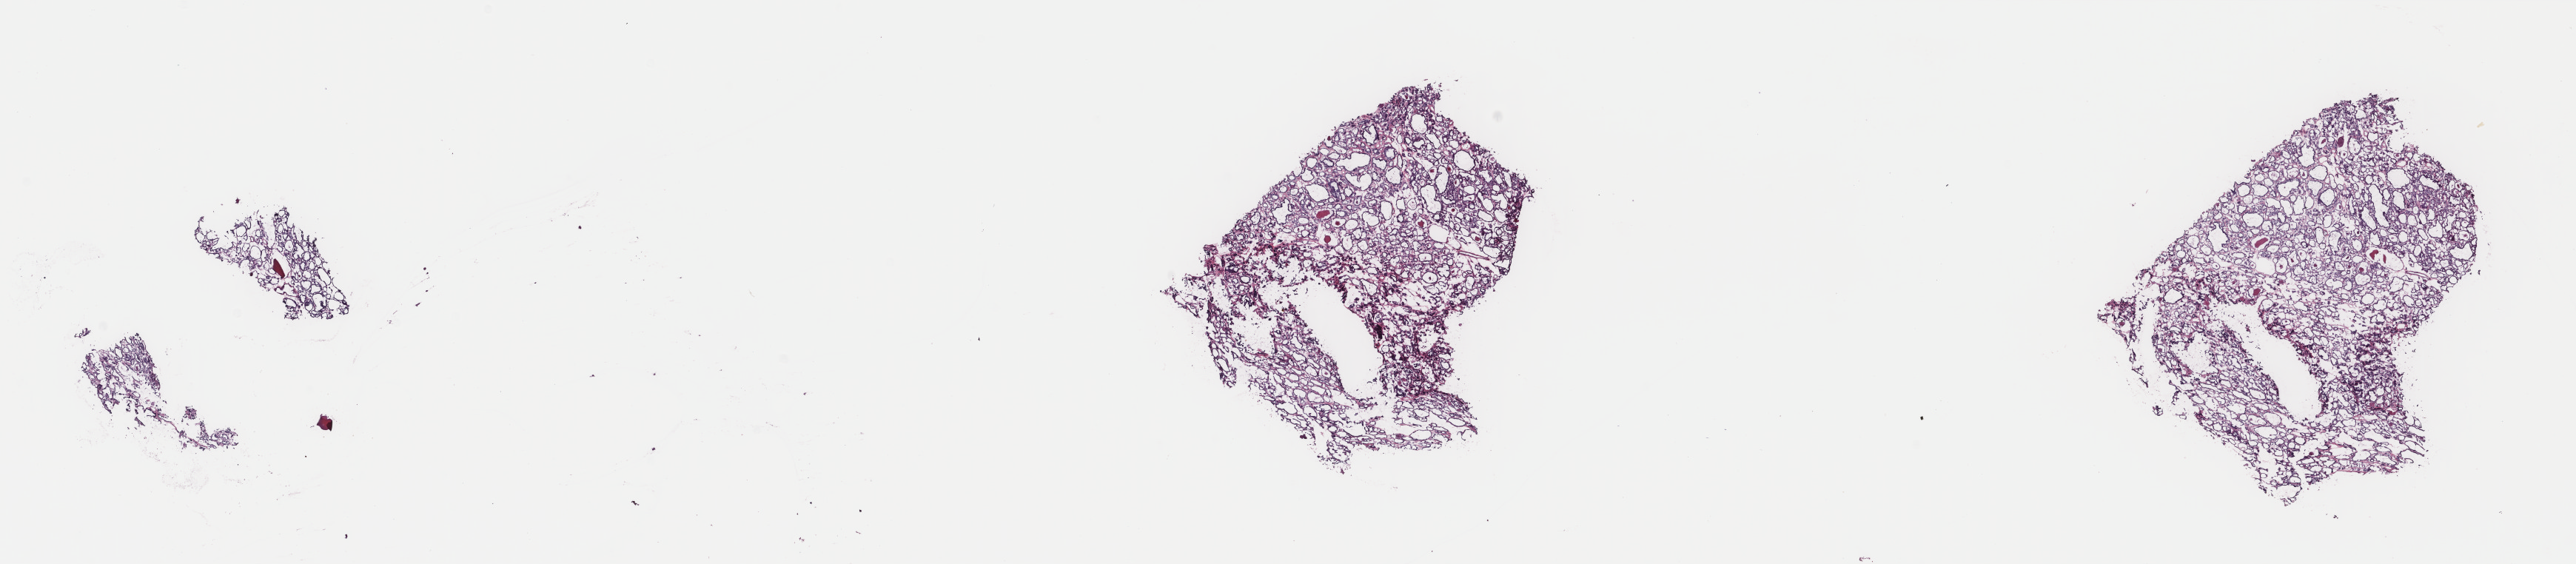
Digitized H&E tissue section (whole slide) — a low-resolution overview of the entire scanned area, about 27.6 x 6.0 mm (acquisition: 40x scan). Frozen section. Thyroid, primary tumour sample. Female patient; age at initial diagnosis 34 years. Composition of this section per pathologist review: tumour cells 99%, tumour nuclei 95%, normal cells 0%, stromal cells 1%, necrosis 0%. Infiltration values recorded for this section: lymphocyte infiltration 0%, monocyte infiltration 0%, neutrophil infiltration 0%.
Pathologic diagnosis: Papillary carcinoma, follicular variant (thyroid gland). Laterality: left. AJCC pathologic stage: I (6th edition).